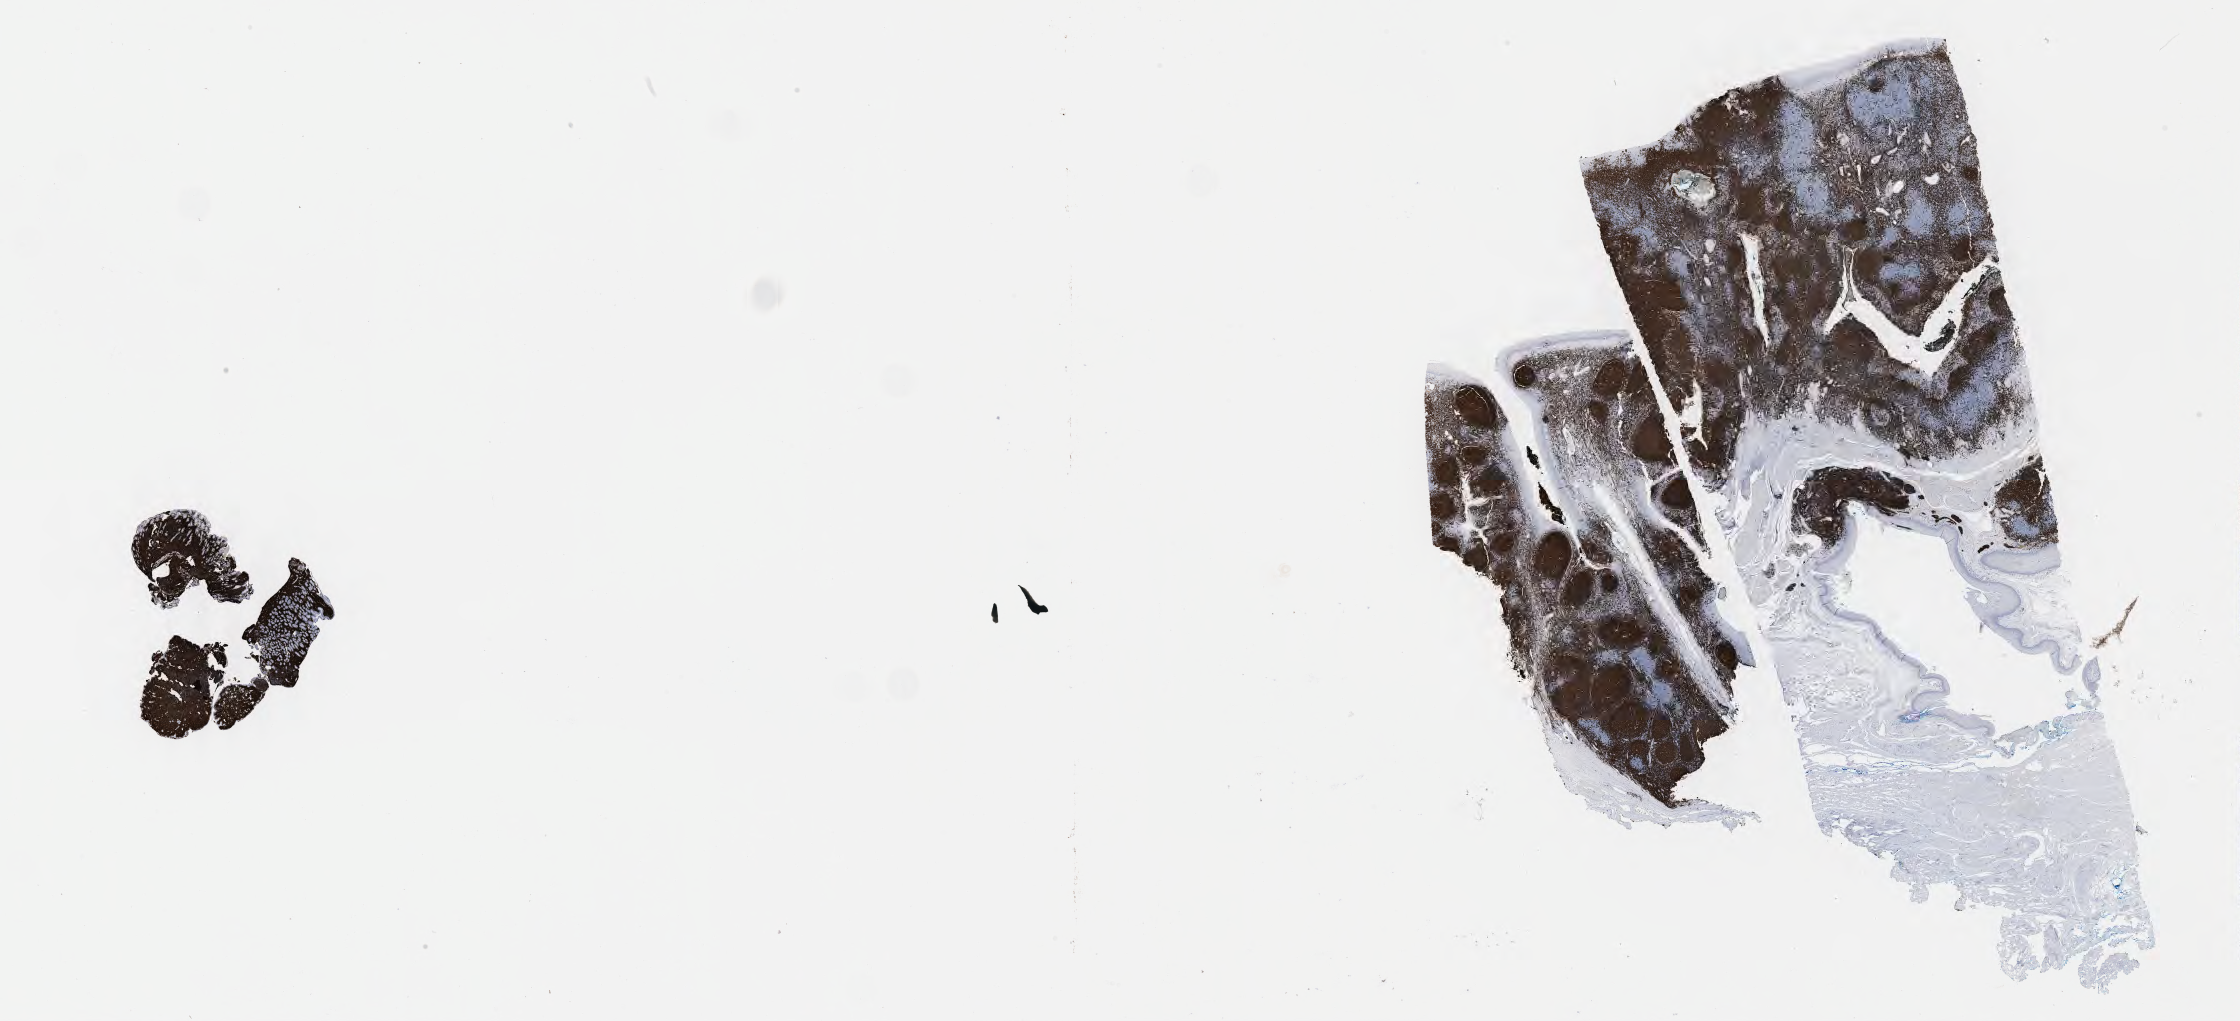
IHC for CD20, whole-slide image, shown as a low-resolution overview of the whole scanned area (about 36.2 x 16.5 mm), specimen: tumor tissue. Patient: female, 45 years old.
Histologic diagnosis: Burkitt lymphoma, NOS.